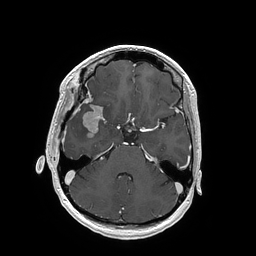
Brain MRI from a brain-tumour surgery series, one axial slice; position 114 of 202 along the scan axis; T1-weighted post-contrast; 1 mm slice thickness; 256 × 256 image matrix, field of view 250 × 250 mm. From the clinical record (not read from this slice): histopathology: Glioblastoma; WHO grade: 4; IDH mutation: no; tumour location: Right Insular.
Outlined on this slice (manually delineated by an expert):
- tumour: bounding box (x1, y1, x2, y2) in pixels: (82, 105, 103, 133)